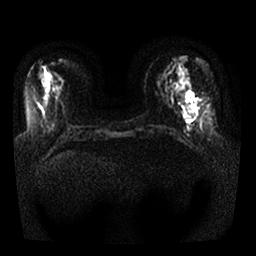
Breast MRI, one axial slice; position 8 of 25 along the scan axis; diffusion-weighted series; image 2 of 4 stored at this slice position (different b-values; order by instance number); 1.5 T; 4 mm slice thickness; 256 × 256 image matrix, field of view 330 × 330 mm. Female patient.
Outlined on this slice (outlined manually by an expert reader):
- tumour on diffusion-weighted imaging: box from (x=186, y=93) to (x=194, y=101) px